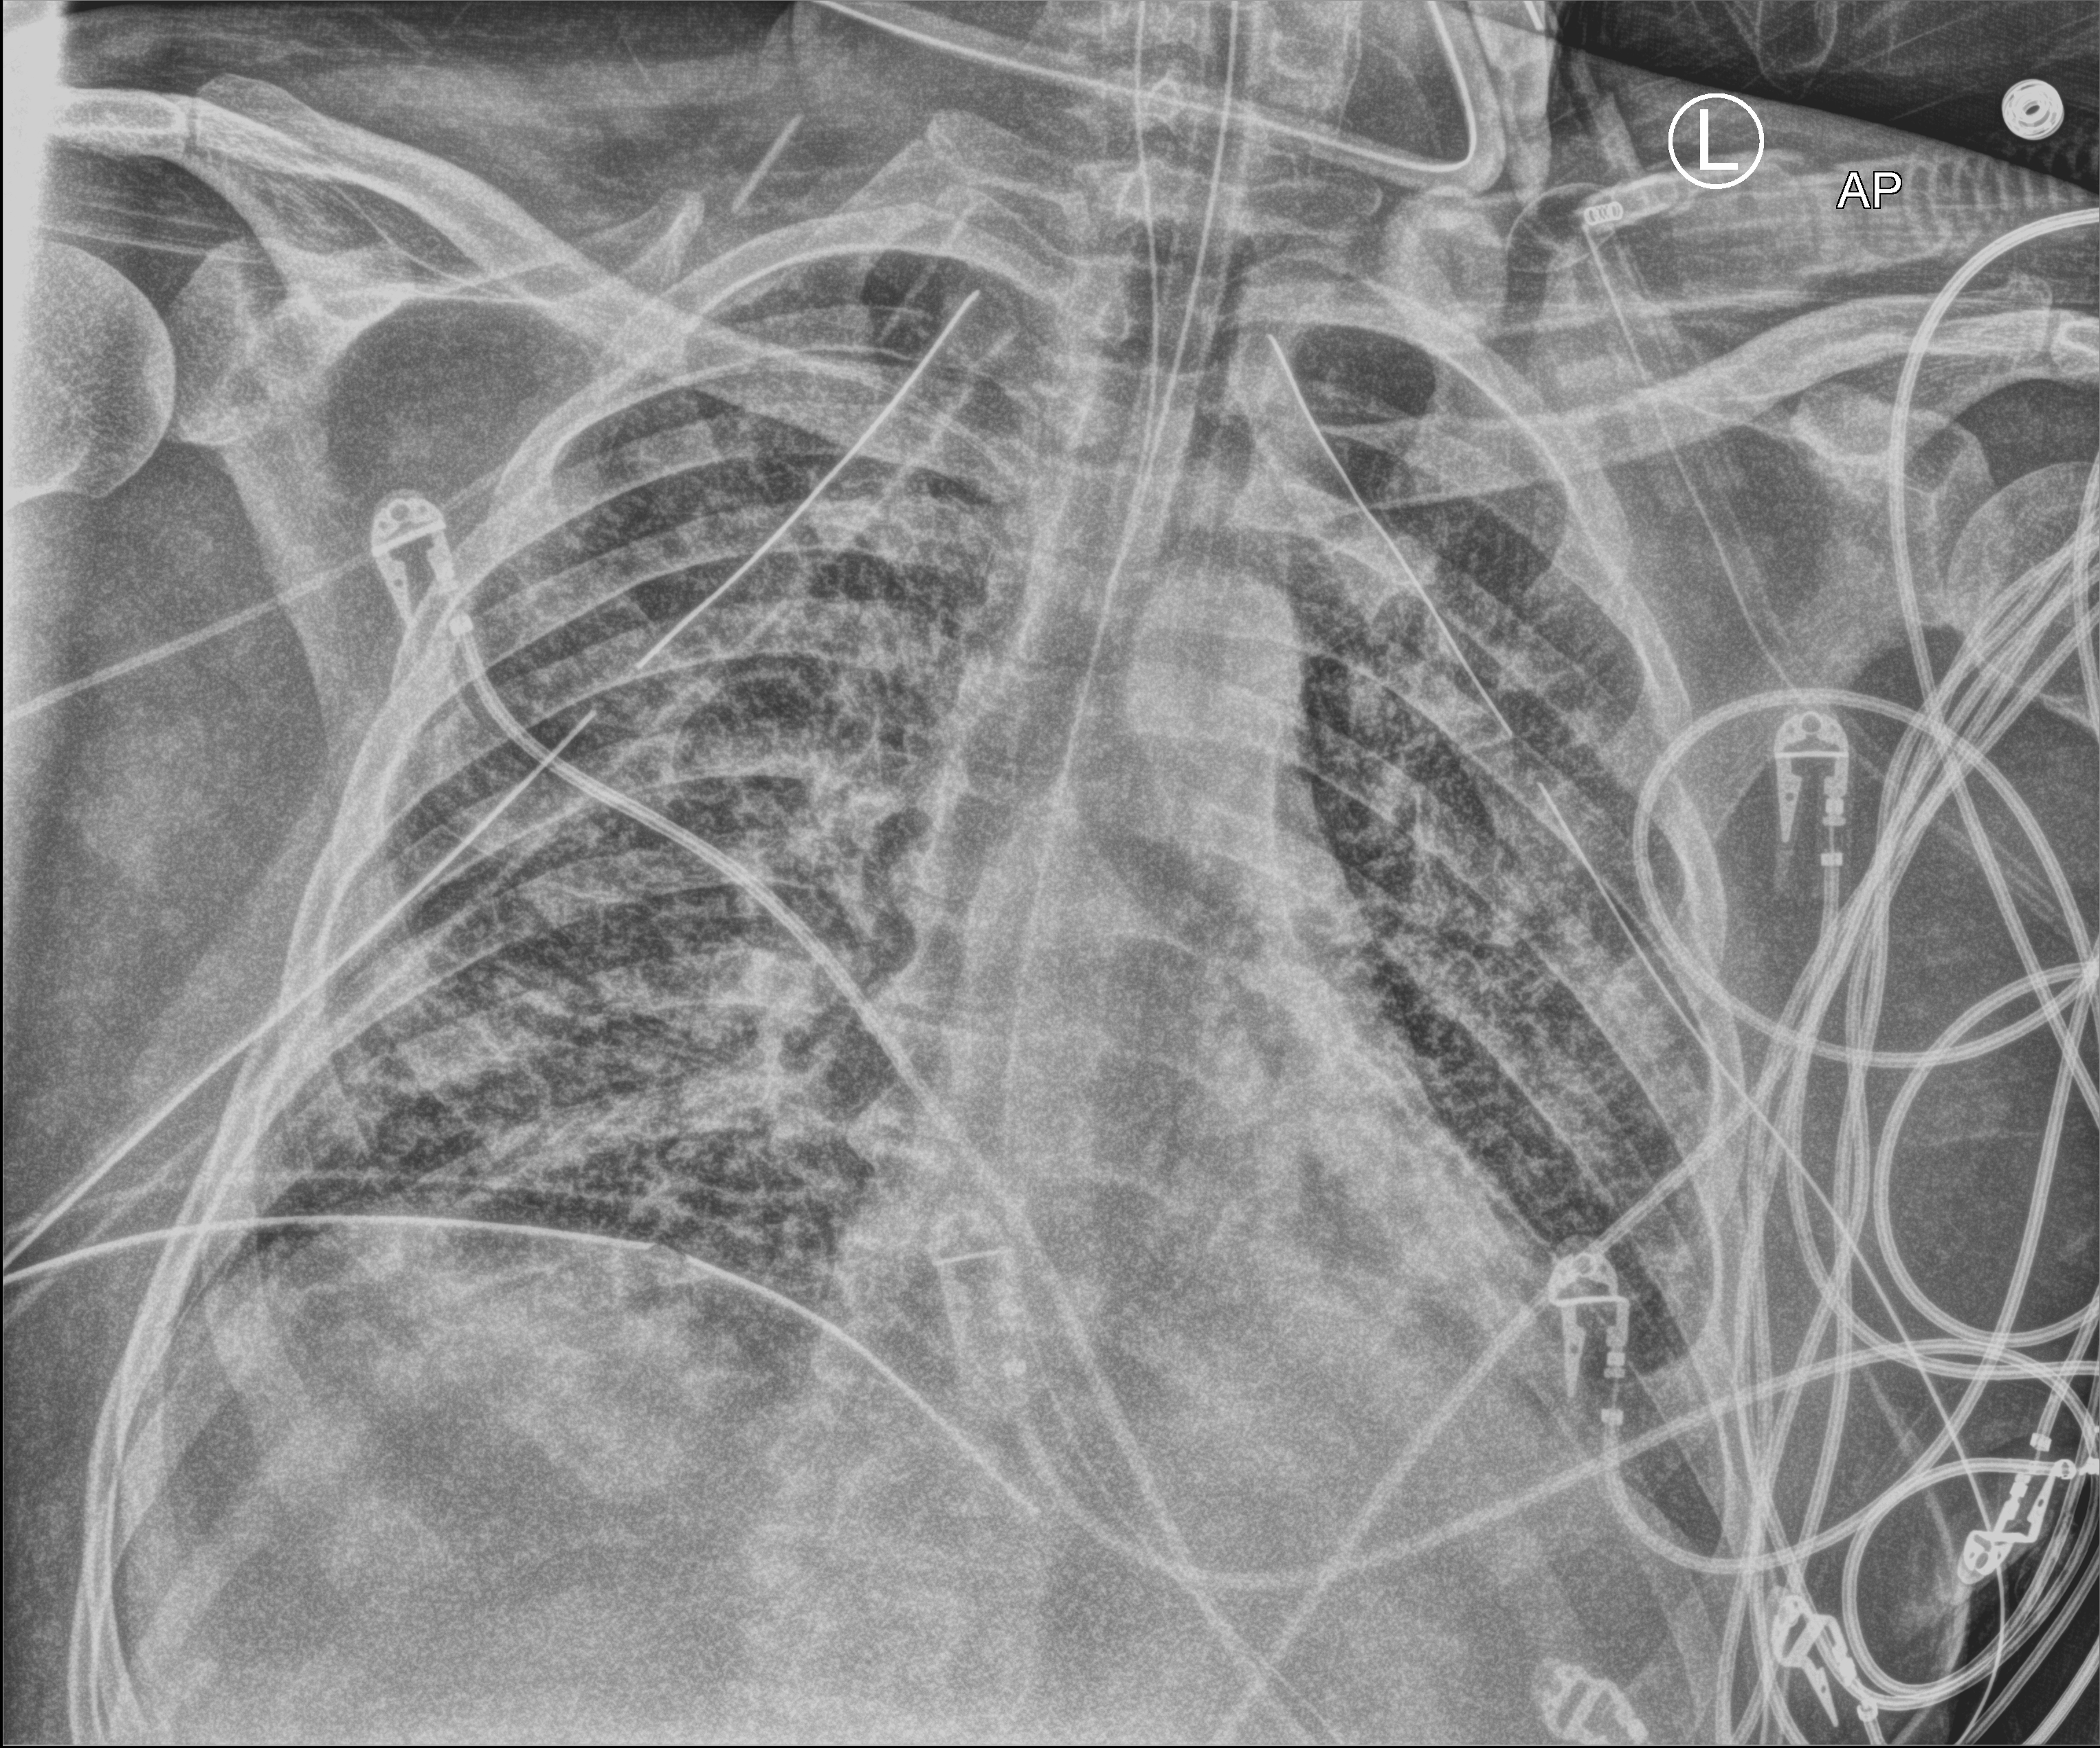
Portable chest radiograph; anteroposterior (AP) projection. Male patient hospitalised with COVID-19, age 18–59 years.
Admission-level facts for this patient (not findings on this image; timing relative to this image not recorded): length of hospital stay: 83 days; mechanically ventilated during this hospital stay: yes.